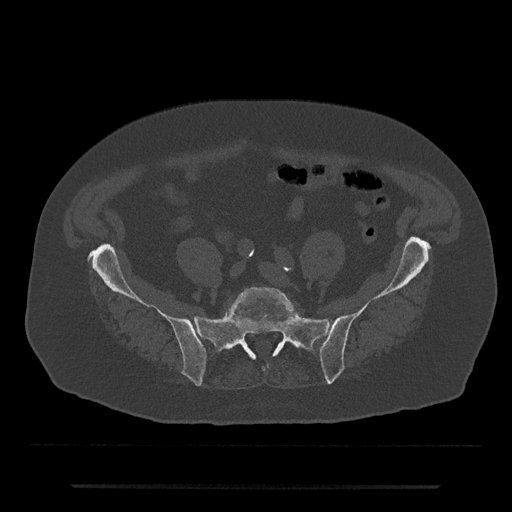
CT including the spine, one axial slice. Slice 251 of 797 in the series (ordered by position). 120 kVp. Bone window (W 1800 / L 400 HU). 0.5 mm slice thickness. 512 × 512 image matrix. Patient: male, 80 years. From the clinical record (not read from this slice): primary cancer: prostate.
Outlined on this slice (semi-automatically segmented with operator editing):
- L5 vertebra: bounding box [x1, y1, x2, y2] px = [226, 287, 298, 350]